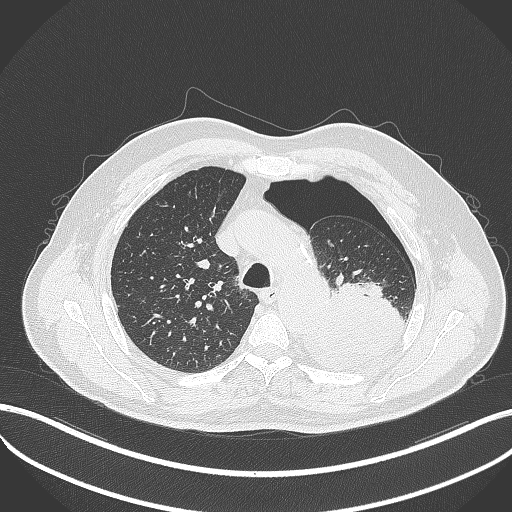
Chest CT, one axial slice; position 376 of 464 along the scan axis; reconstruction kernel B70f; 120 kVp; lung window (W 1500 / L -600 HU); 512 × 512 image matrix. Male patient, age 76 years. From the clinical record (not read from this slice): clinical TNM (as recorded): T3 N0 M1b.
Annotated regions visible in this slice (rectangle marked by the reading radiologist):
- lung tumour (recorded histology: adenocarcinoma): bounding box [x1, y1, x2, y2] px = [296, 282, 412, 377]